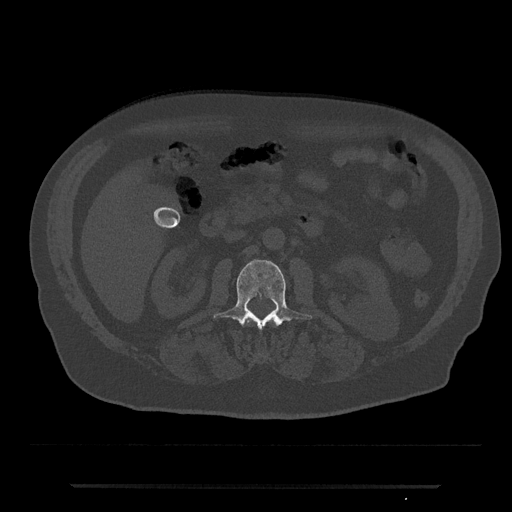
CT including the spine, one axial slice. Position 478 of 797 along the scan axis. 120 kVp. Bone window (W 1800 / L 400 HU). 512 × 512 image matrix. Male patient, age 80 years. From the clinical record (not read from this slice): primary cancer: prostate.
Structures marked on this image (semi-automatic segmentation, software-assisted and operator-edited):
- L1 vertebra: bounding box <244,320,277,326> (left, top, right, bottom; pixels)
- L2 vertebra: <214,259,312,331>